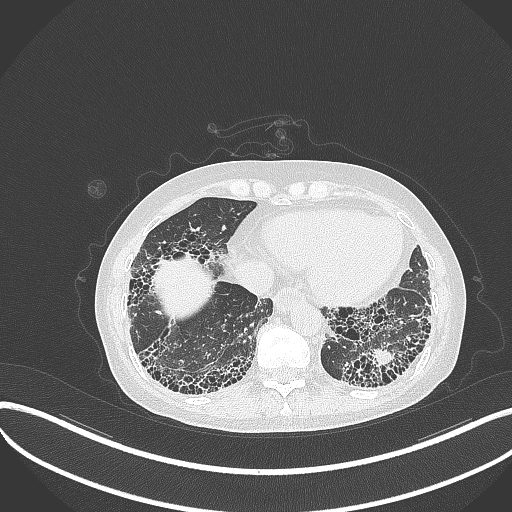
Chest CT, one axial slice; position 73 of 373 along the scan axis; reconstruction kernel B70f; 120 kVp; lung window (W 1500 / L -600 HU); 512 × 512 image matrix, field of view 400 × 400 mm. Female patient, age 56 years. From the clinical record (not read from this slice): clinical TNM (as recorded): T1 N0 M0.
Outlined on this slice (rectangle marked by the reading radiologist):
- lung tumour (recorded histology: adenocarcinoma): bounding box [x1, y1, x2, y2] px = [368, 346, 398, 371]